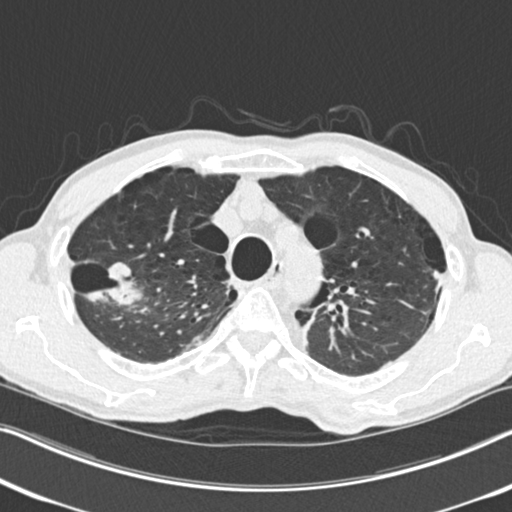
Chest CT (low-dose screening protocol), one axial image, second screening round (one year after baseline), lung window (W 1500 / L -600 HU), standard (soft-tissue) reconstruction kernel (B30f), 120 kVp, slice 58 of 251 in the series, 512 × 512 image matrix, field of view 334 × 334 mm. Male participant, aged 71 years at enrolment.
- Expert reader's lesion annotation, box from (x=73, y=251) to (x=147, y=319) px.
- The screening reader recorded 4 non-calcified nodules or masses ≥4 mm on this exam; which of them this box marks is not recorded.
- Official screen result: positive, change unspecified: nodule(s) >= 4 mm or enlarging nodule(s), mass(es), or other non-specific abnormalities suspicious for lung cancer.
- Participant outcome: lung cancer diagnosed 83 days after this screen — adenocarcinoma, NOS, right upper lobe, well differentiated (G1), stage IA (AJCC 6th edition), 30 mm at pathology.